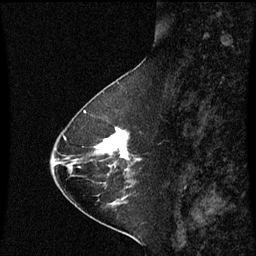
Breast MRI (dynamic contrast-enhanced), one sagittal slice. Position 23 of 60 along the scan axis. Dynamic contrast-enhanced series, image 2 of 3 at this slice position (ordered by acquisition). 1.5 T. TE 4.2 ms, TR 8.9 ms. 256 × 256 image matrix. Female patient, age 63 years. From the clinical record (not read from this slice): setting: breast cancer imaged before/during neoadjuvant chemotherapy; receptor status: HR-positive, HER2-negative.
Outlined on this slice (semi-automatically segmented with operator editing):
- analysis volume of interest (the breast-tissue region the enhancement analysis was run in; not a lesion): box from (x=94, y=128) to (x=142, y=177) px
- tumour enhancement mask (voxels above the 70 % enhancement threshold inside the analysis volume of interest): (x=97, y=128)–(x=129, y=159)